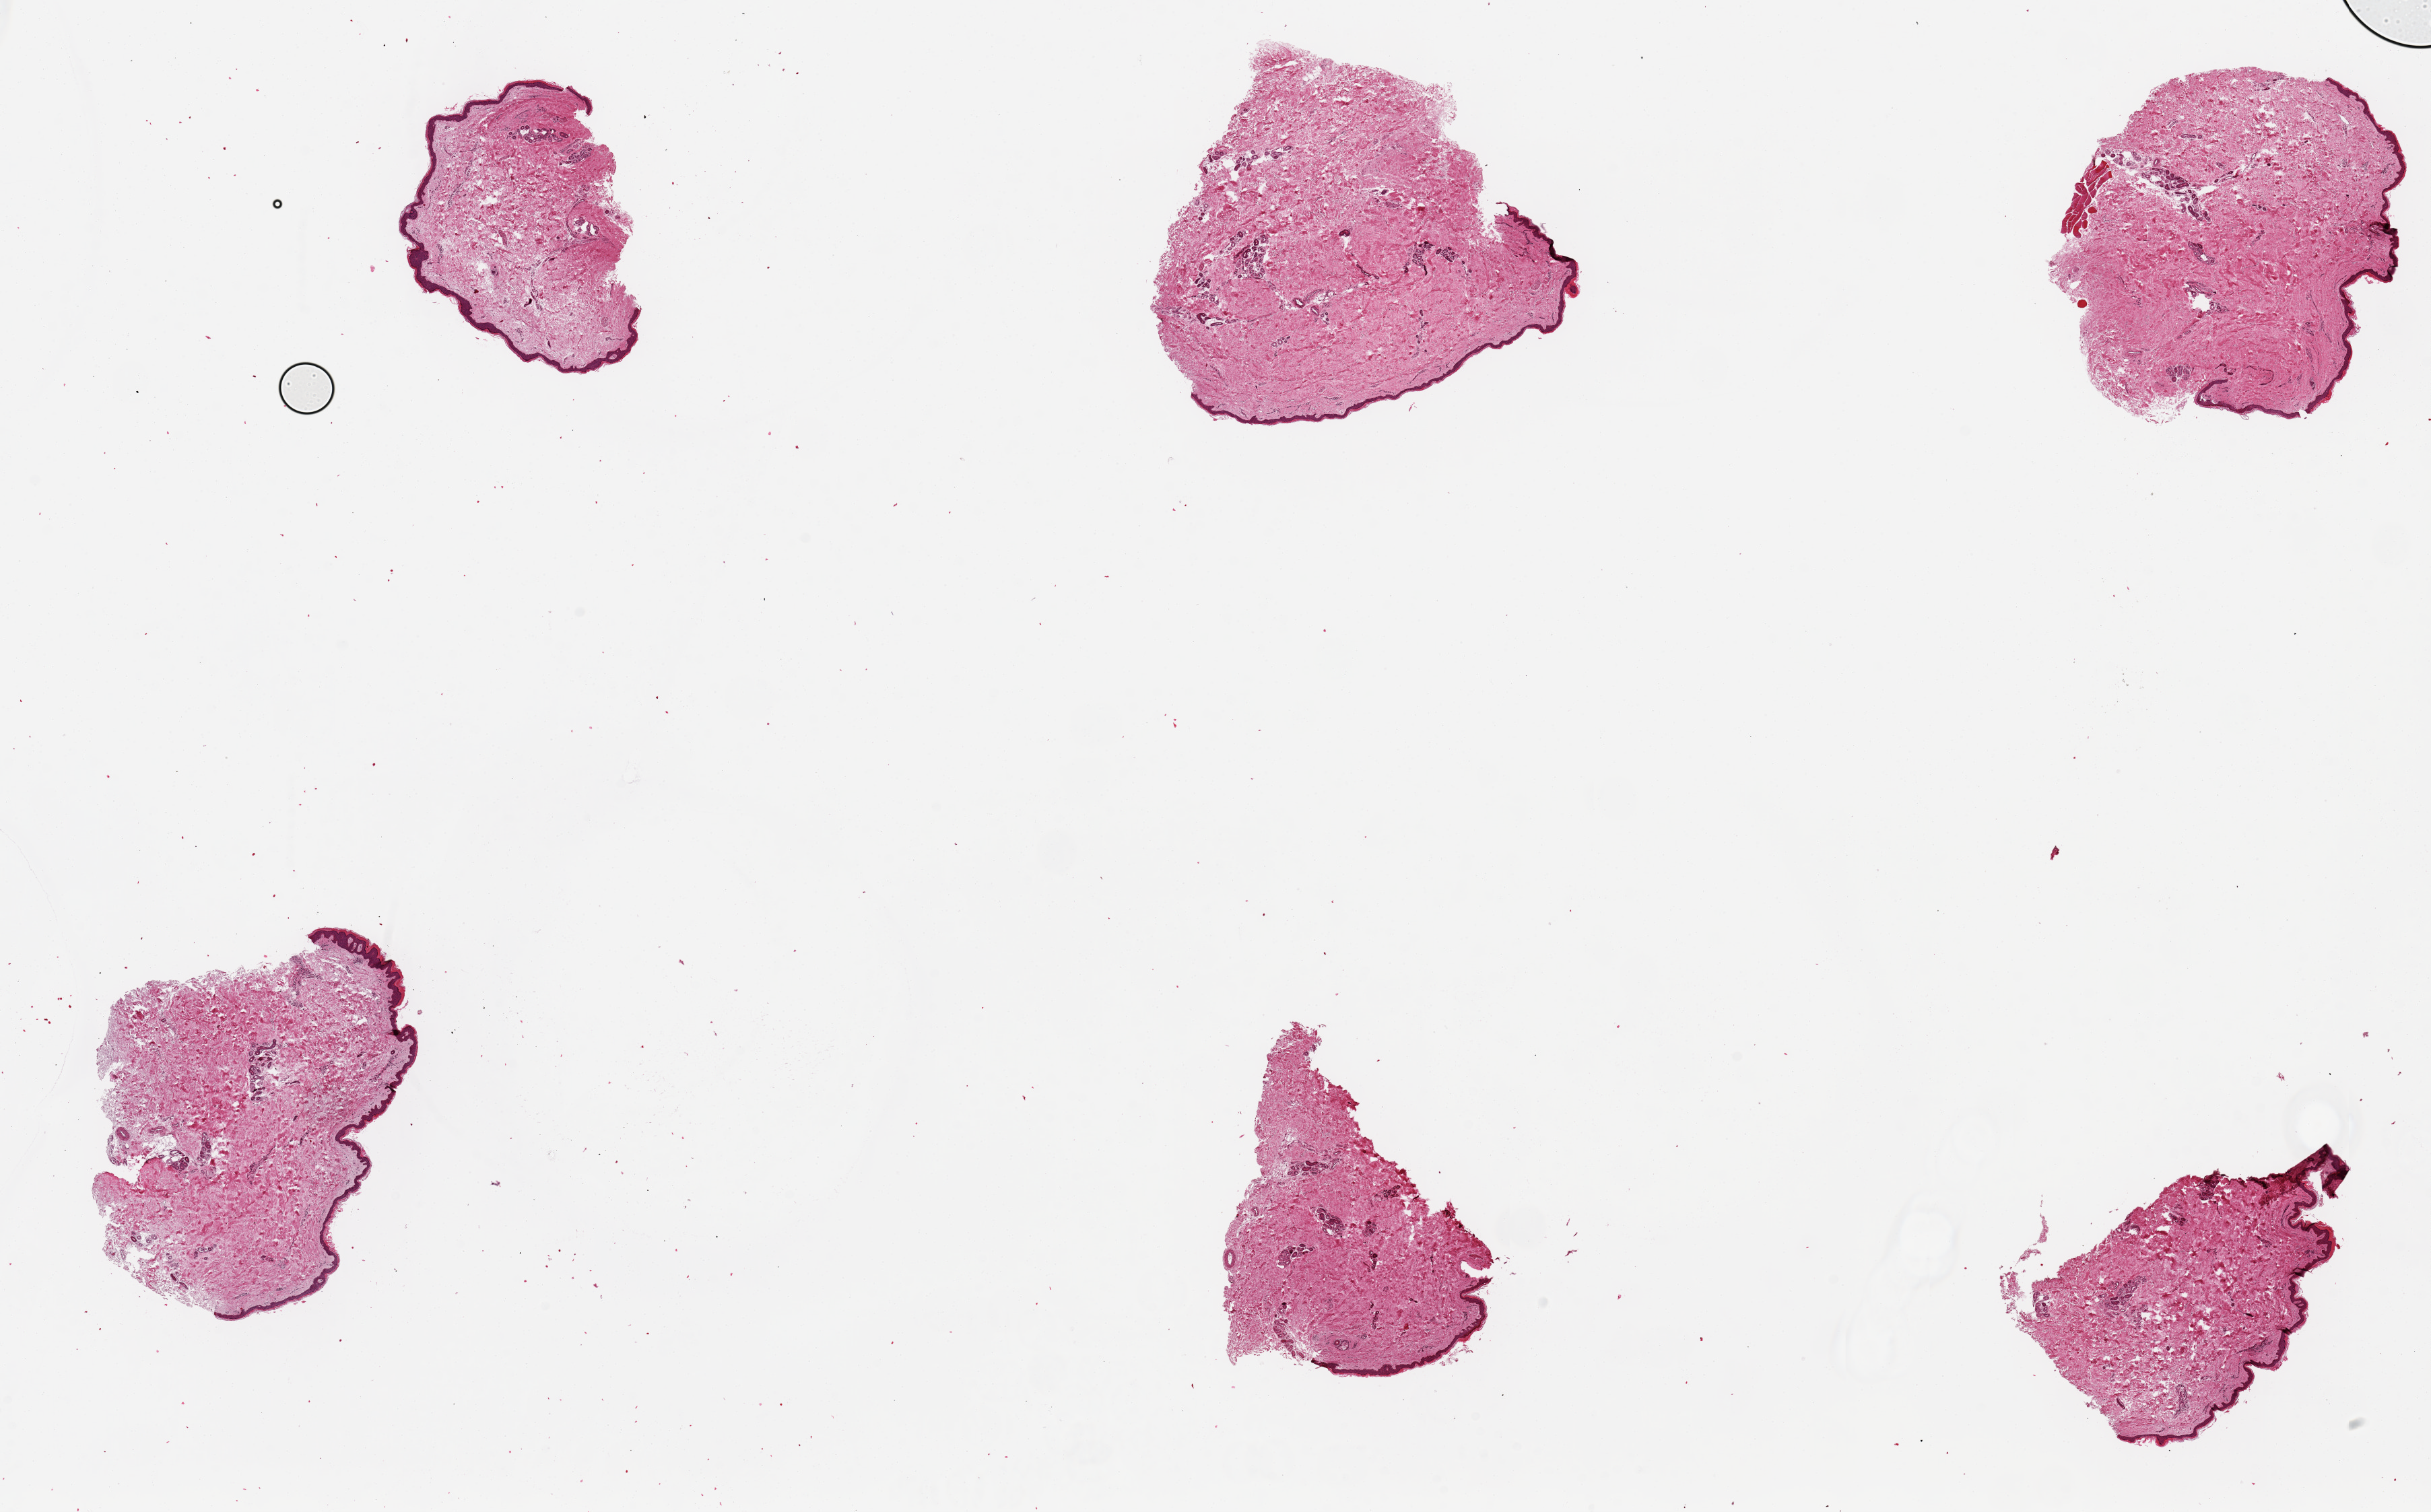
Digitized haematoxylin and eosin-stained section, brightfield — a low-resolution overview of the entire scanned area, about 28.5 x 17.8 mm; PAXgene-fixed, paraffin-embedded tissue; sampled site (target tissue): skin of lower leg; tissue donor sample. Male donor.
- reviewer comment on this tissue sample: 6 pieces. up to 5x4.5mm; well trimmed